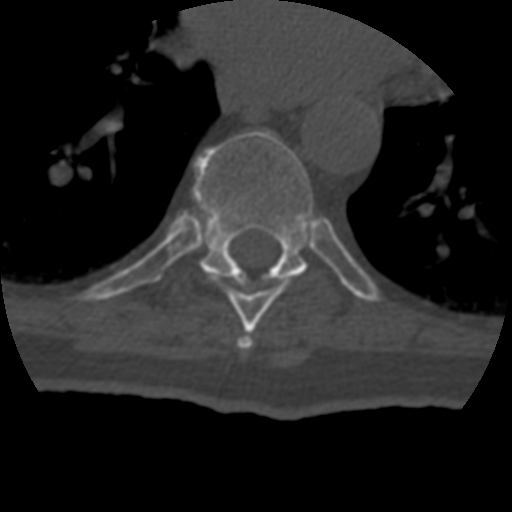
CT including the spine, one axial slice; slice 249 of 399 in the series (ordered by position); reconstruction kernel STANDARD; bone window (W 1800 / L 400 HU); 1.25 mm slice thickness; 512 × 512 image matrix, field of view 160 × 160 mm. Patient age 69 years. Case-level facts recorded for this patient, not image findings: primary cancer: prostate.
Outlined on this slice (semi-automatically segmented with operator editing):
- T7 vertebra: bounding box <237,336,253,349> (left, top, right, bottom; pixels)
- T8 vertebra: <212,273,289,333>
- T9 vertebra: <194,131,337,310>